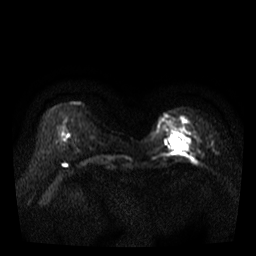
Breast MRI, one axial slice; position 11 of 35 along the scan axis; diffusion-weighted series; image 2 of 4 stored at this slice position (different b-values; order by instance number); 3 T; 5 mm slice thickness; 256 × 256 image matrix. Female patient.
Outlined on this slice (manually delineated by an expert):
- tumour on diffusion-weighted imaging: bounding box (x1, y1, x2, y2) in pixels: (169, 136, 191, 151)